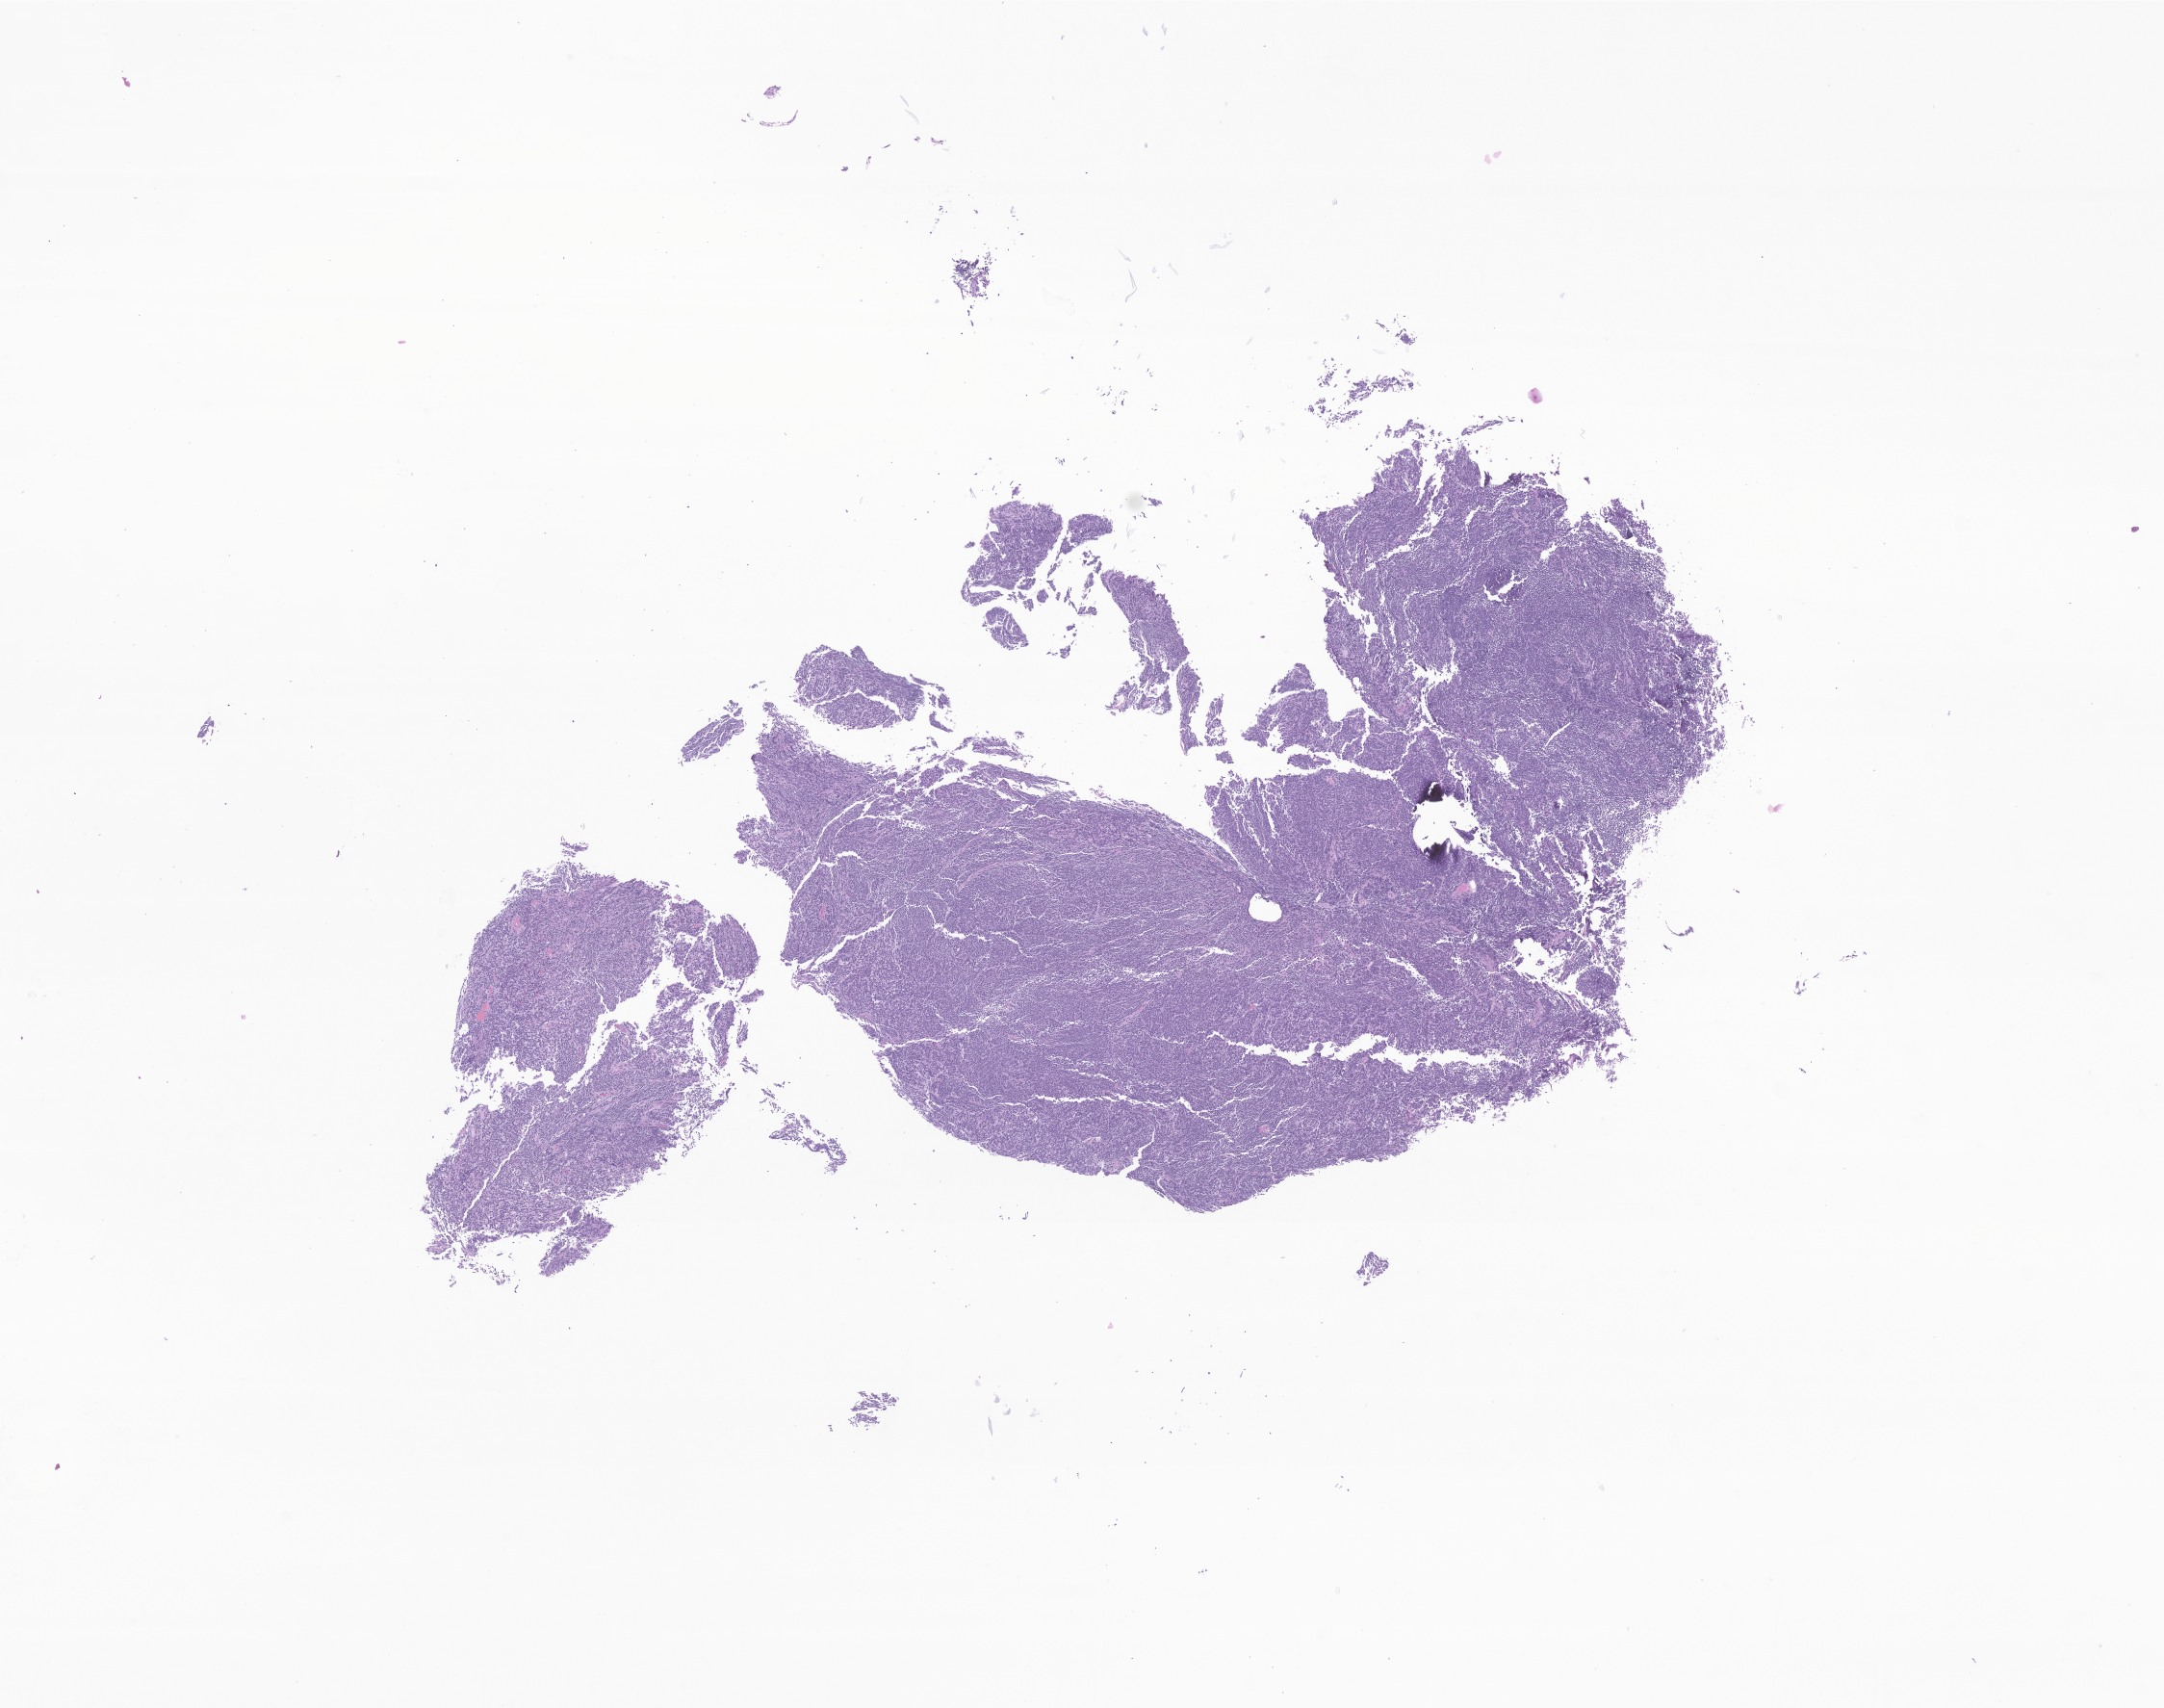
Hematoxylin and eosin (H&E) whole-slide image of tumor tissue from the brain, shown as a low-resolution overview of the whole scanned area (about 9.5 x 7.5 mm), formalin-fixed paraffin-embedded section. Patient: male, age 278 months (23 years 2 months).
Diagnosis: Medulloblastoma, NOS.